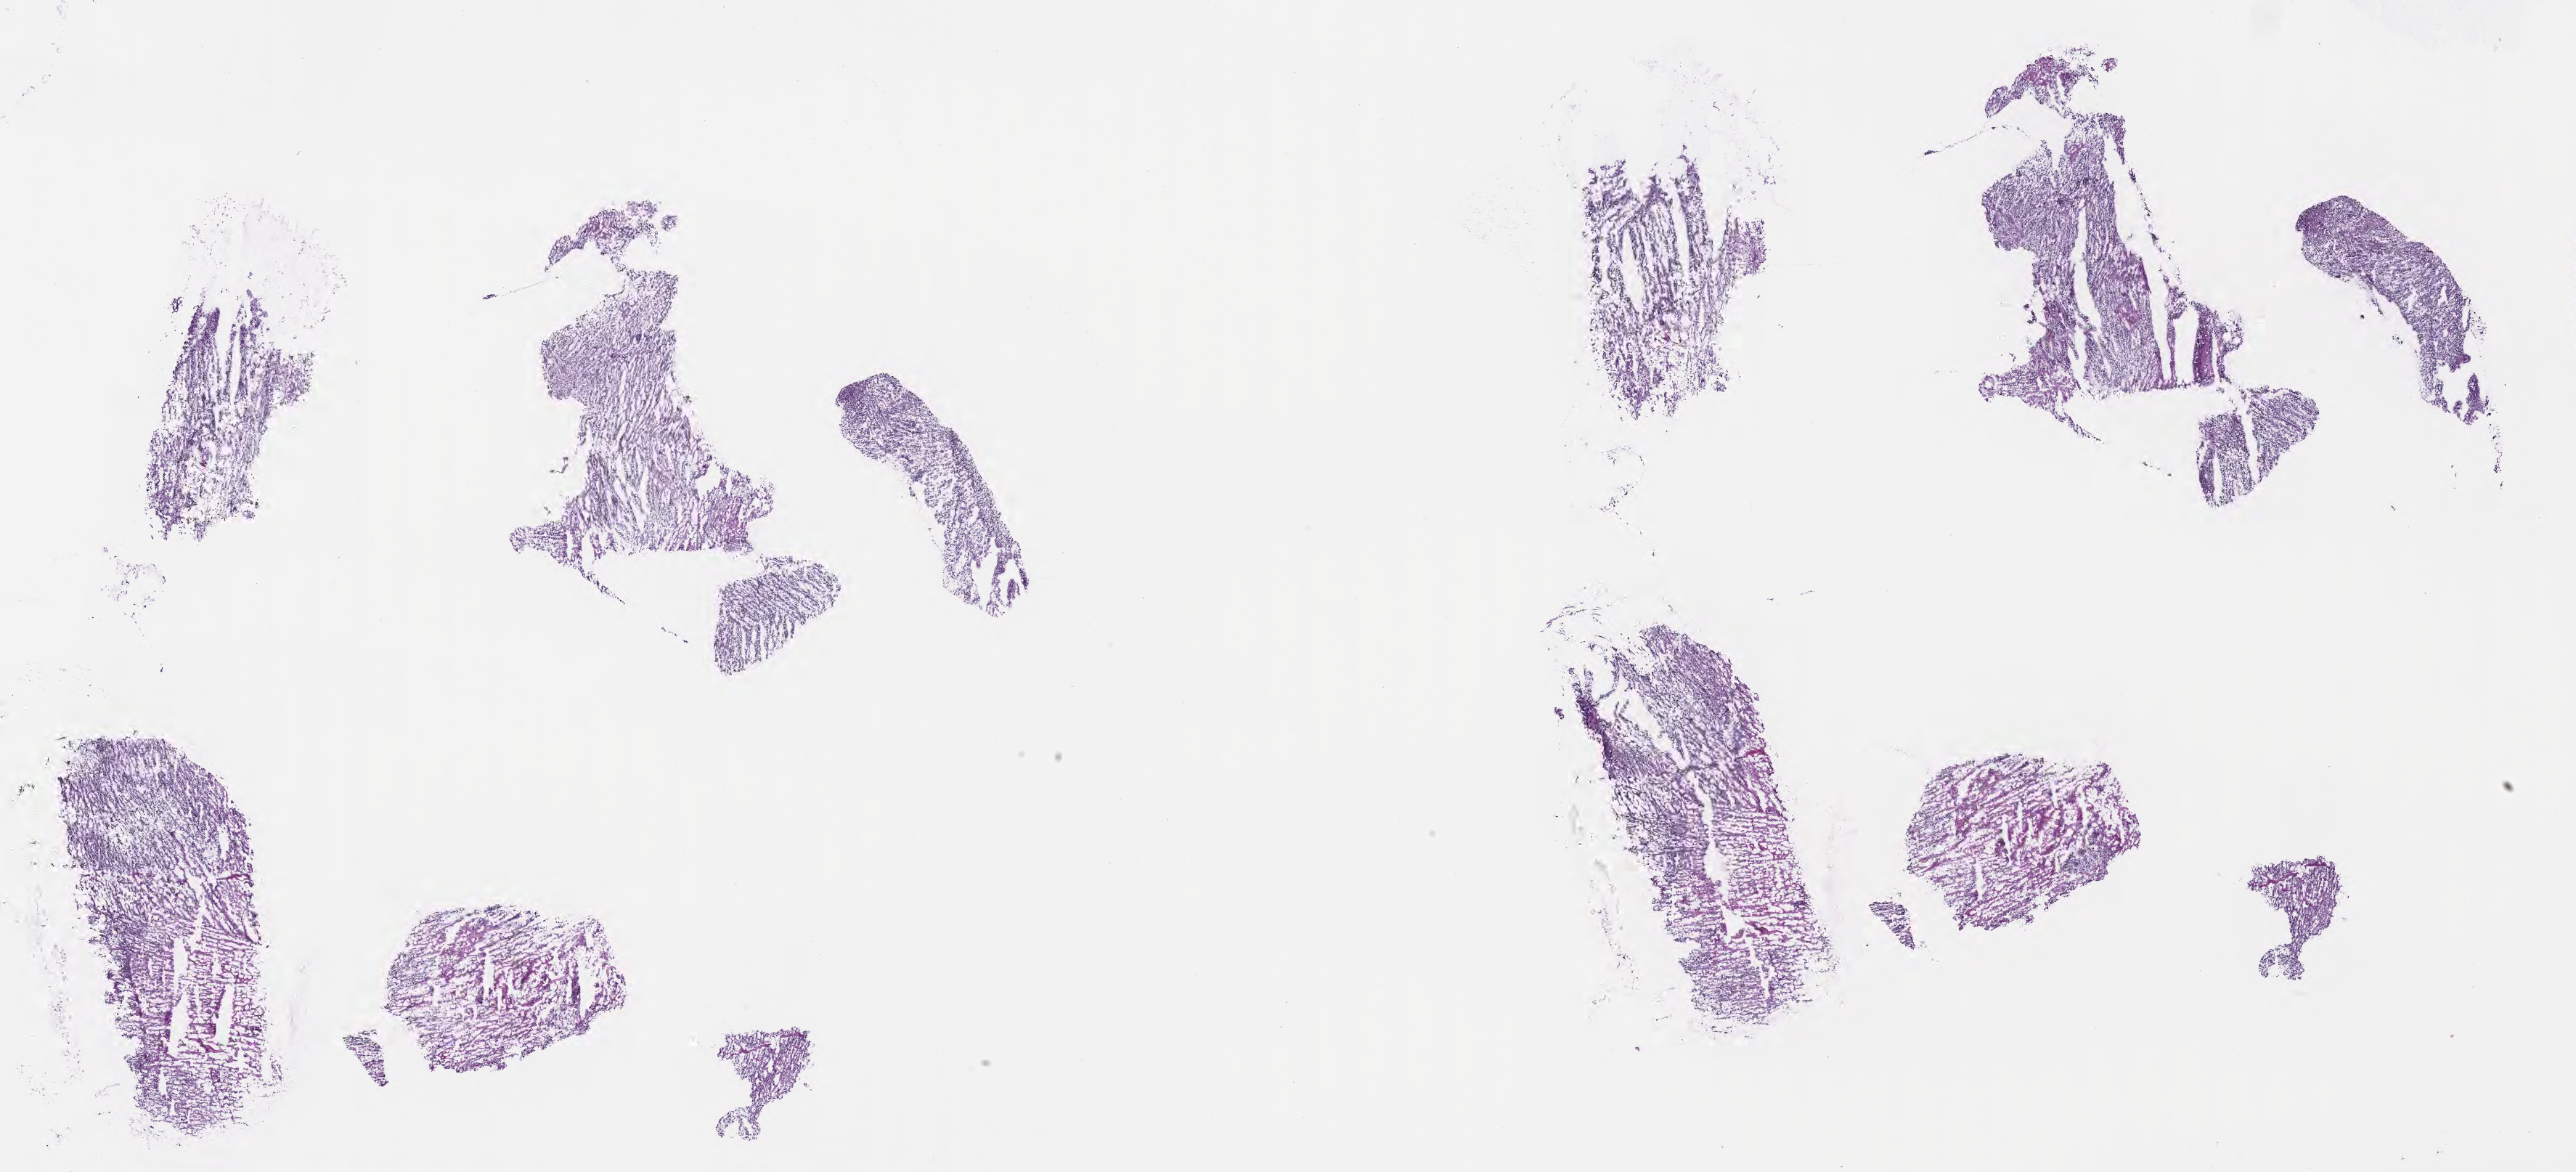
Digitized H&E-stained section — whole scanned area (about 28.7 x 13.0 mm) shown as a low-resolution overview, frozen section, specimen: primary tumor, site: brain. Female patient; age at initial diagnosis 11 years. Pathologist review of this section (percent, as recorded): tumor cells 68%, tumor nuclei 86%, stromal cells 1%, necrosis 20%, normal cells 11%. Infiltration values recorded for this section: lymphocyte infiltration 0%, monocyte infiltration 0%, neutrophil infiltration 0%.
Diagnosis: Glioblastoma, NOS. Section: top of the tissue portion.